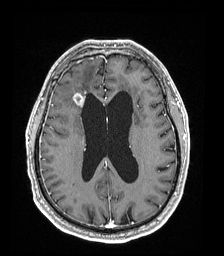
Brain MRI from a brain-tumour surgery series, one axial slice. Slice 77 of 192 in the series (ordered by position). T1-weighted post-contrast. 1 mm slice thickness. 224 × 256 image matrix. From the clinical record (not read from this slice): histopathology: Astrocytoma; WHO grade: 4; IDH mutation: yes.
Structures marked on this image (outlined manually by an expert reader):
- tumour: bounding box <73,93,84,105> (left, top, right, bottom; pixels)